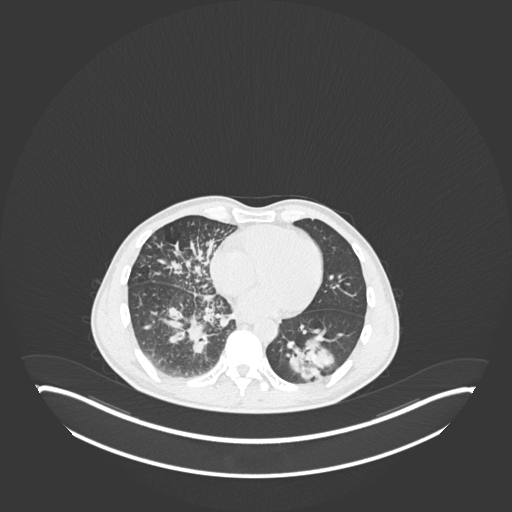
Chest CT, one axial slice; position 88 of 237 along the scan axis; lung window (W 1500 / L -600 HU); 1 mm slice thickness; 512 × 512 image matrix. Male patient, age 49 years. Case-level facts recorded for this patient, not image findings: clinical TNM (as recorded): T2b N1 M0.
Annotated regions visible in this slice (bounding box drawn by a radiologist):
- lung tumour (recorded histology: adenocarcinoma): bounding box <286,335,339,385> (left, top, right, bottom; pixels)